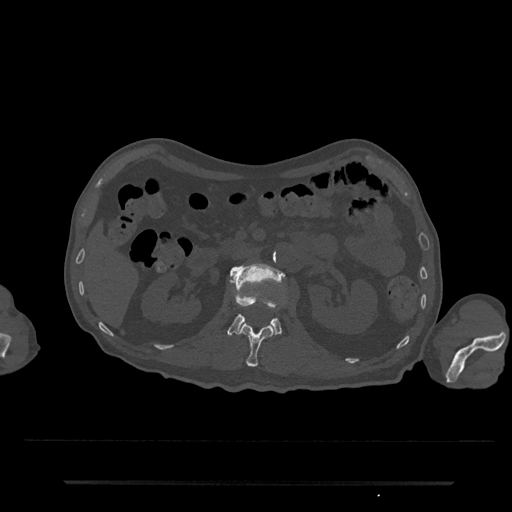
CT including the spine, one axial slice. Position 99 of 797 along the scan axis. 120 kVp. Bone window (W 1800 / L 400 HU). 0.5 mm slice thickness. 512 × 512 image matrix. Patient: male, 74 years. From the clinical record (not read from this slice): primary cancer: prostate.
Structures marked on this image (semi-automatically segmented with operator editing):
- L1 vertebra: bounding box <239,323,274,367> (left, top, right, bottom; pixels)
- L2 vertebra: <227,262,283,335>